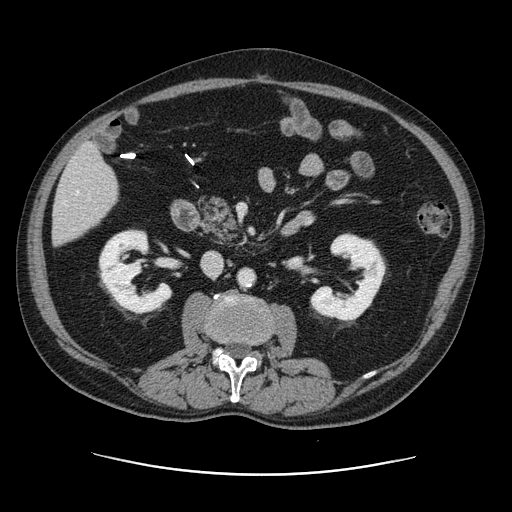
Contrast-enhanced abdominal CT, one axial slice; position 42 of 141 along the scan axis; 120 kVp; intravenous contrast given; soft-tissue window (W 400 / L 40 HU); 2.5 mm slice thickness; 512 × 512 image matrix, field of view 395 × 395 mm. Male patient, age 72 years. From the clinical record (not read from this slice): diagnosis: colorectal cancer liver metastases, imaged before liver resection; multiple liver metastases: yes; largest metastasis: 5.4 cm; chemotherapy before resection: yes.
Structures marked on this image (manually delineated by an expert):
- hepatic veins: box from (x=63, y=190) to (x=79, y=204) px
- liver: (x=54, y=145)–(x=118, y=245)
- planned liver remnant (the part of the liver to remain after resection): (x=54, y=150)–(x=118, y=245)